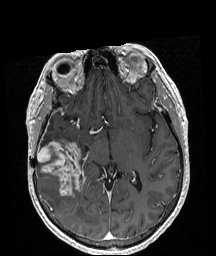
Brain MRI from a brain-tumour surgery series, one axial slice. Position 110 of 208 along the scan axis. T1-weighted post-contrast. 216 × 256 image matrix. From the clinical record (not read from this slice): histopathology: Astrocytoma; WHO grade: 4; IDH mutation: yes.
Annotated regions visible in this slice (manually delineated by an expert):
- tumour: bounding box <37,141,81,196> (left, top, right, bottom; pixels)